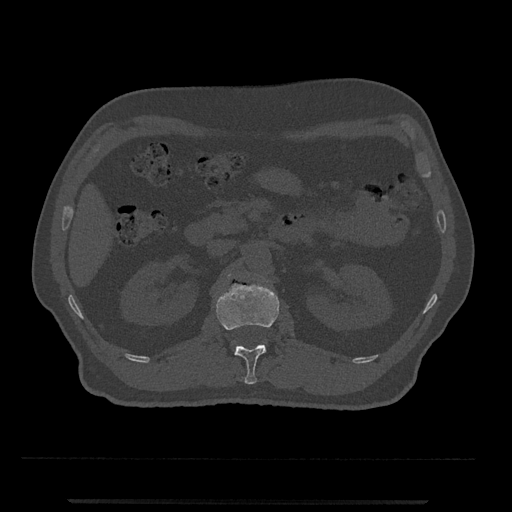
CT including the spine, one axial slice. Slice 317 of 797 in the series (ordered by position). Reconstruction kernel Br40s/3. 120 kVp. Bone window (W 1800 / L 400 HU). 0.5 mm slice thickness. 512 × 512 image matrix. Male patient, age 63 years. Case-level facts recorded for this patient, not image findings: primary cancer: prostate.
Outlined on this slice (semi-automatic segmentation, software-assisted and operator-edited):
- L1 vertebra: box from (x=216, y=283) to (x=280, y=384) px
- L2 vertebra: (x=228, y=274)–(x=231, y=277)